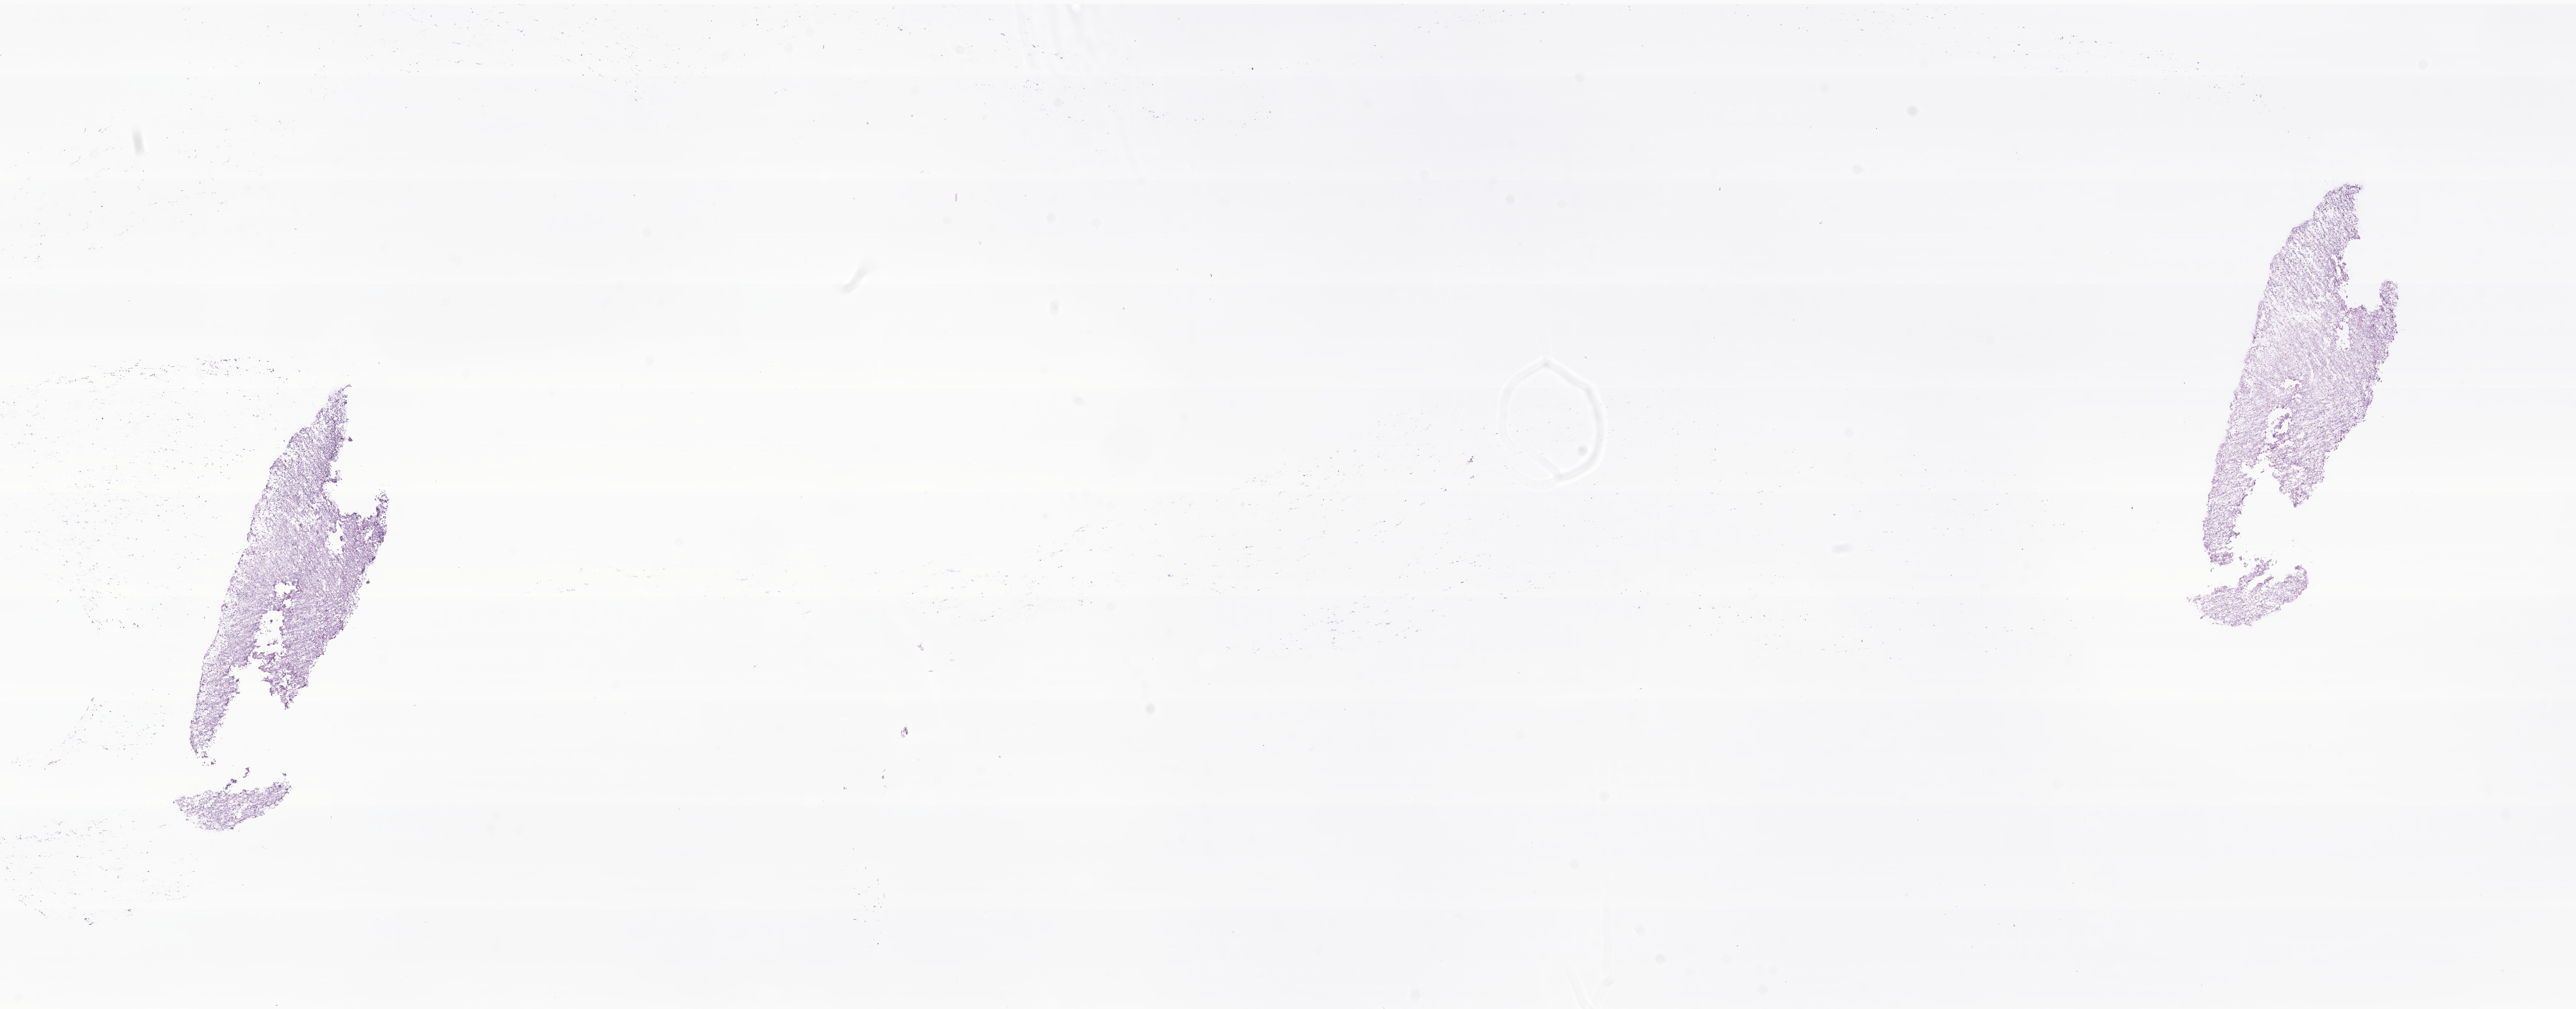
Whole-slide image, haematoxylin and eosin stain of tumor tissue from the parietal lobe — a low-resolution overview of the entire scanned area, about 26.4 x 10.3 mm. Frozen section. Patient: male, age 93 months (7 years 9 months).
* recorded diagnosis: CNS embryonal tumor, NOS